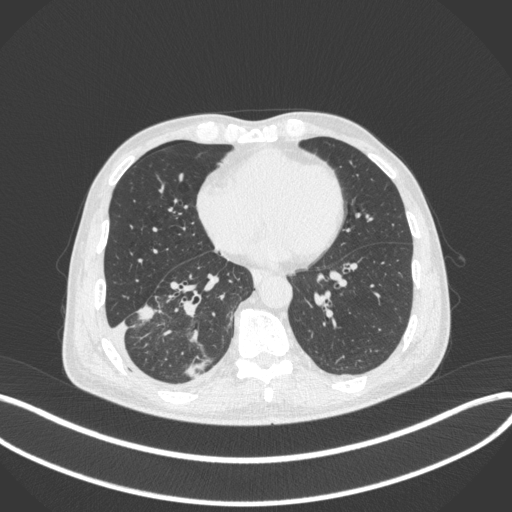
Chest CT, one axial slice; slice 147 of 385 in the series (ordered by position); reconstruction kernel B31f; 120 kVp; lung window (W 1500 / L -600 HU); 1 mm slice thickness; 512 × 512 image matrix. Patient: male, 64 years. From the clinical record (not read from this slice): clinical TNM (as recorded): T3 N0 M0; histopathological grade: G2-3.
Outlined on this slice (rectangle marked by the reading radiologist):
- lung tumour (recorded histology: adenocarcinoma): box from (x=135, y=300) to (x=161, y=327) px